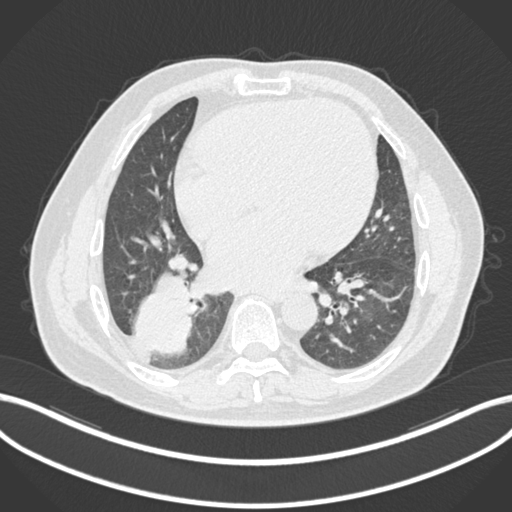
Chest CT, one axial slice. Slice 66 of 200 in the series (ordered by position). Lung window (W 1500 / L -600 HU). 512 × 512 image matrix. Patient: male, 59 years.
Annotated regions visible in this slice (rectangle marked by the reading radiologist):
- lung tumour (recorded histology: adenocarcinoma): box from (x=129, y=273) to (x=197, y=361) px